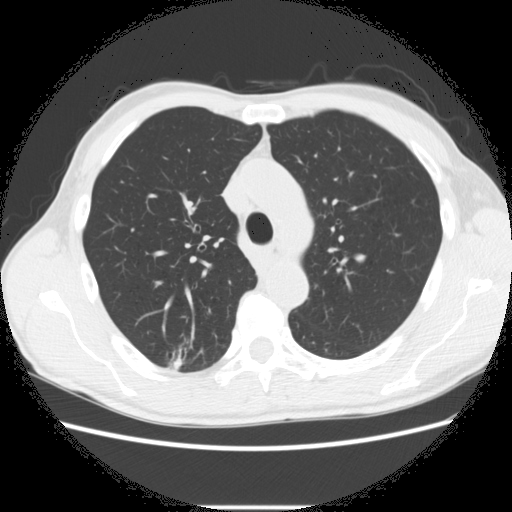
Low-dose screening chest CT, one axial slice; reconstruction kernel STANDARD; lung window (W 1500 / L -600 HU); 2.5 mm slice thickness; 512 × 512 image matrix, field of view 360 × 360 mm.
Structures marked on this image (expert manual segmentation):
- lesion 1 (tumor, upper lobe of right lung): bounding box [x1, y1, x2, y2] px = [171, 357, 184, 370]